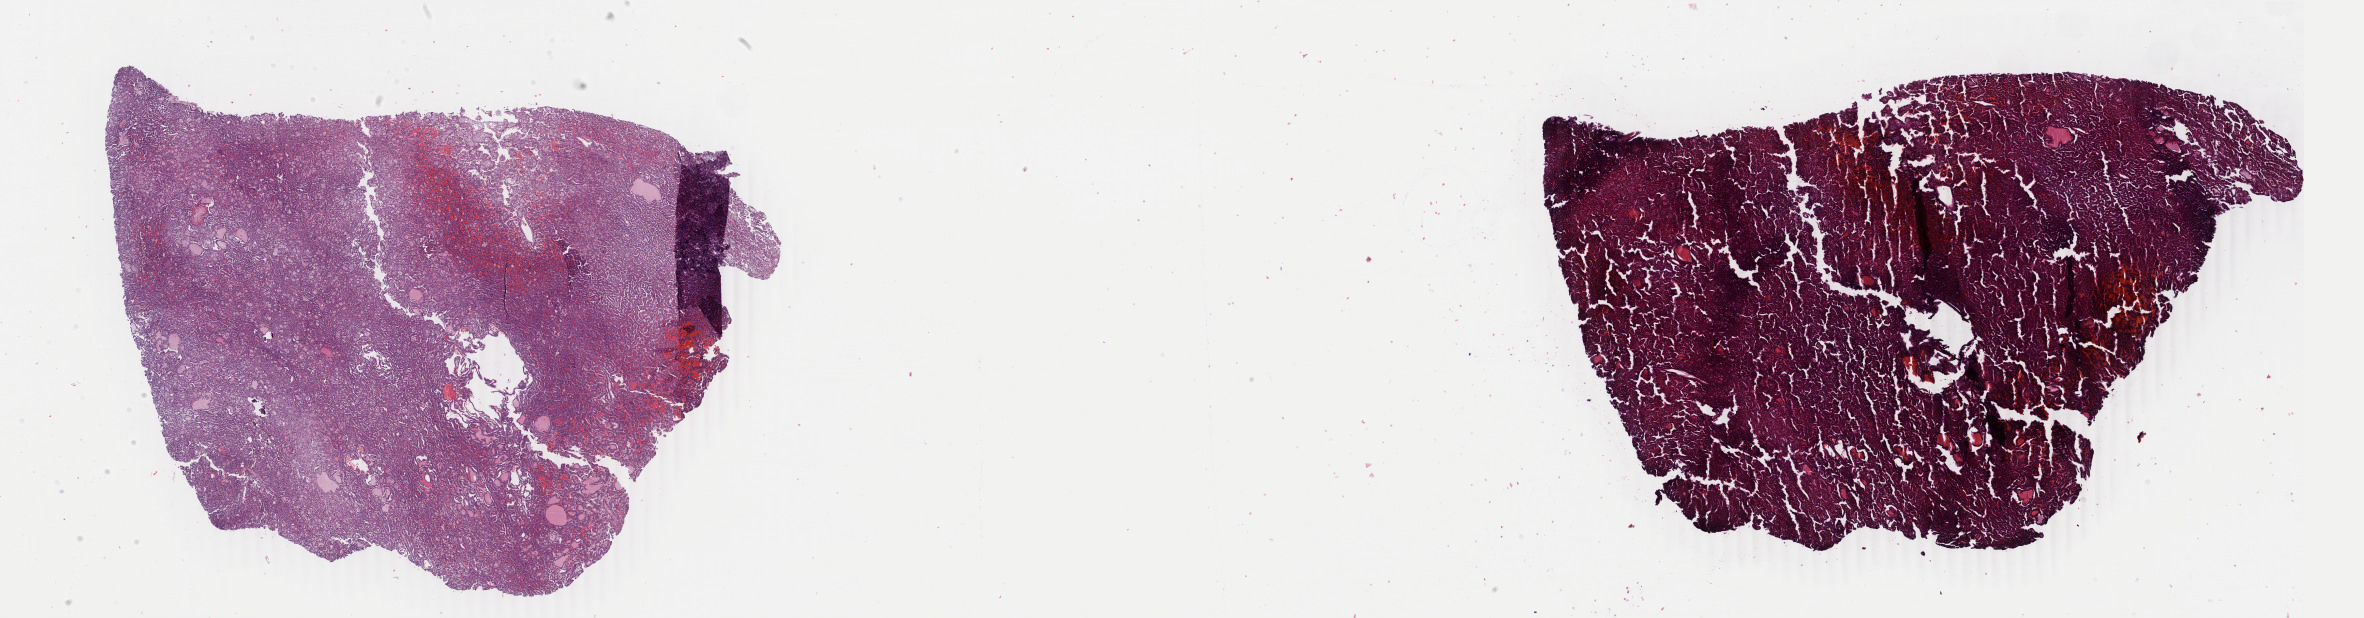
H&E whole-slide image, a low-resolution overview of the entire scanned area, about 37.6 x 9.8 mm (acquisition: 40x scan), formalin-fixed paraffin-embedded (FFPE) diagnostic section, kidney, primary tumour sample. Patient: male, age at initial diagnosis 46 years.
AJCC pathologic stage: I (7th edition). Diagnosis: Papillary adenocarcinoma, NOS.